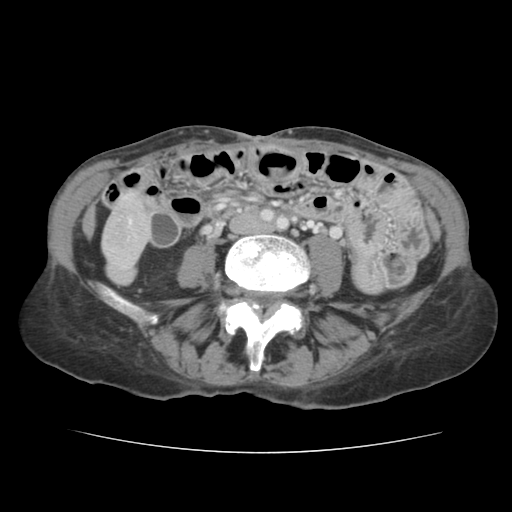
Contrast-enhanced abdominal CT, one axial slice; slice 18 of 136 in the series (ordered by position); 120 kVp; intravenous contrast given; soft-tissue window (W 400 / L 40 HU); 512 × 512 image matrix, field of view 319 × 319 mm. Female patient, age 77 years. From the clinical record (not read from this slice): diagnosis: colorectal cancer liver metastases, imaged before liver resection; multiple liver metastases: yes; largest metastasis: 3 cm; disease in both lobes: no.
Annotated regions visible in this slice (outlined manually by an expert reader):
- liver: bounding box (x1, y1, x2, y2) in pixels: (104, 196, 148, 275)